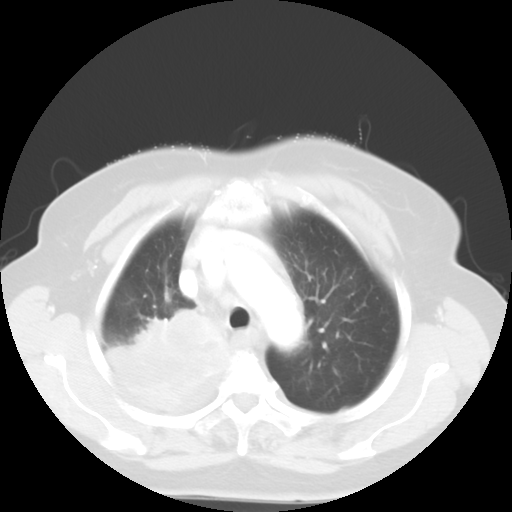
Chest CT, one axial slice; slice 42 of 52 in the series (ordered by position); 120 kVp; lung window (W 1500 / L -600 HU); 512 × 512 image matrix, field of view 333 × 333 mm. Patient: female, 81 years. From the clinical record (not read from this slice): clinical TNM (as recorded): T4 N3 M1b.
Annotated regions visible in this slice (rectangle marked by the reading radiologist):
- lung tumour (recorded histology: adenocarcinoma): bounding box (x1, y1, x2, y2) in pixels: (107, 309, 231, 413)